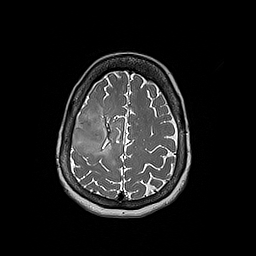
Brain MRI from a brain-tumour surgery series, one axial slice. Position 57 of 192 along the scan axis. 256 × 256 image matrix, field of view 250 × 250 mm. From the clinical record (not read from this slice): histopathology: Oligodendroglioma; WHO grade: 3; IDH mutation: yes; tumour location: Right Frontal.
Structures marked on this image (outlined manually by an expert reader):
- tumour: bounding box <71,114,106,153> (left, top, right, bottom; pixels)